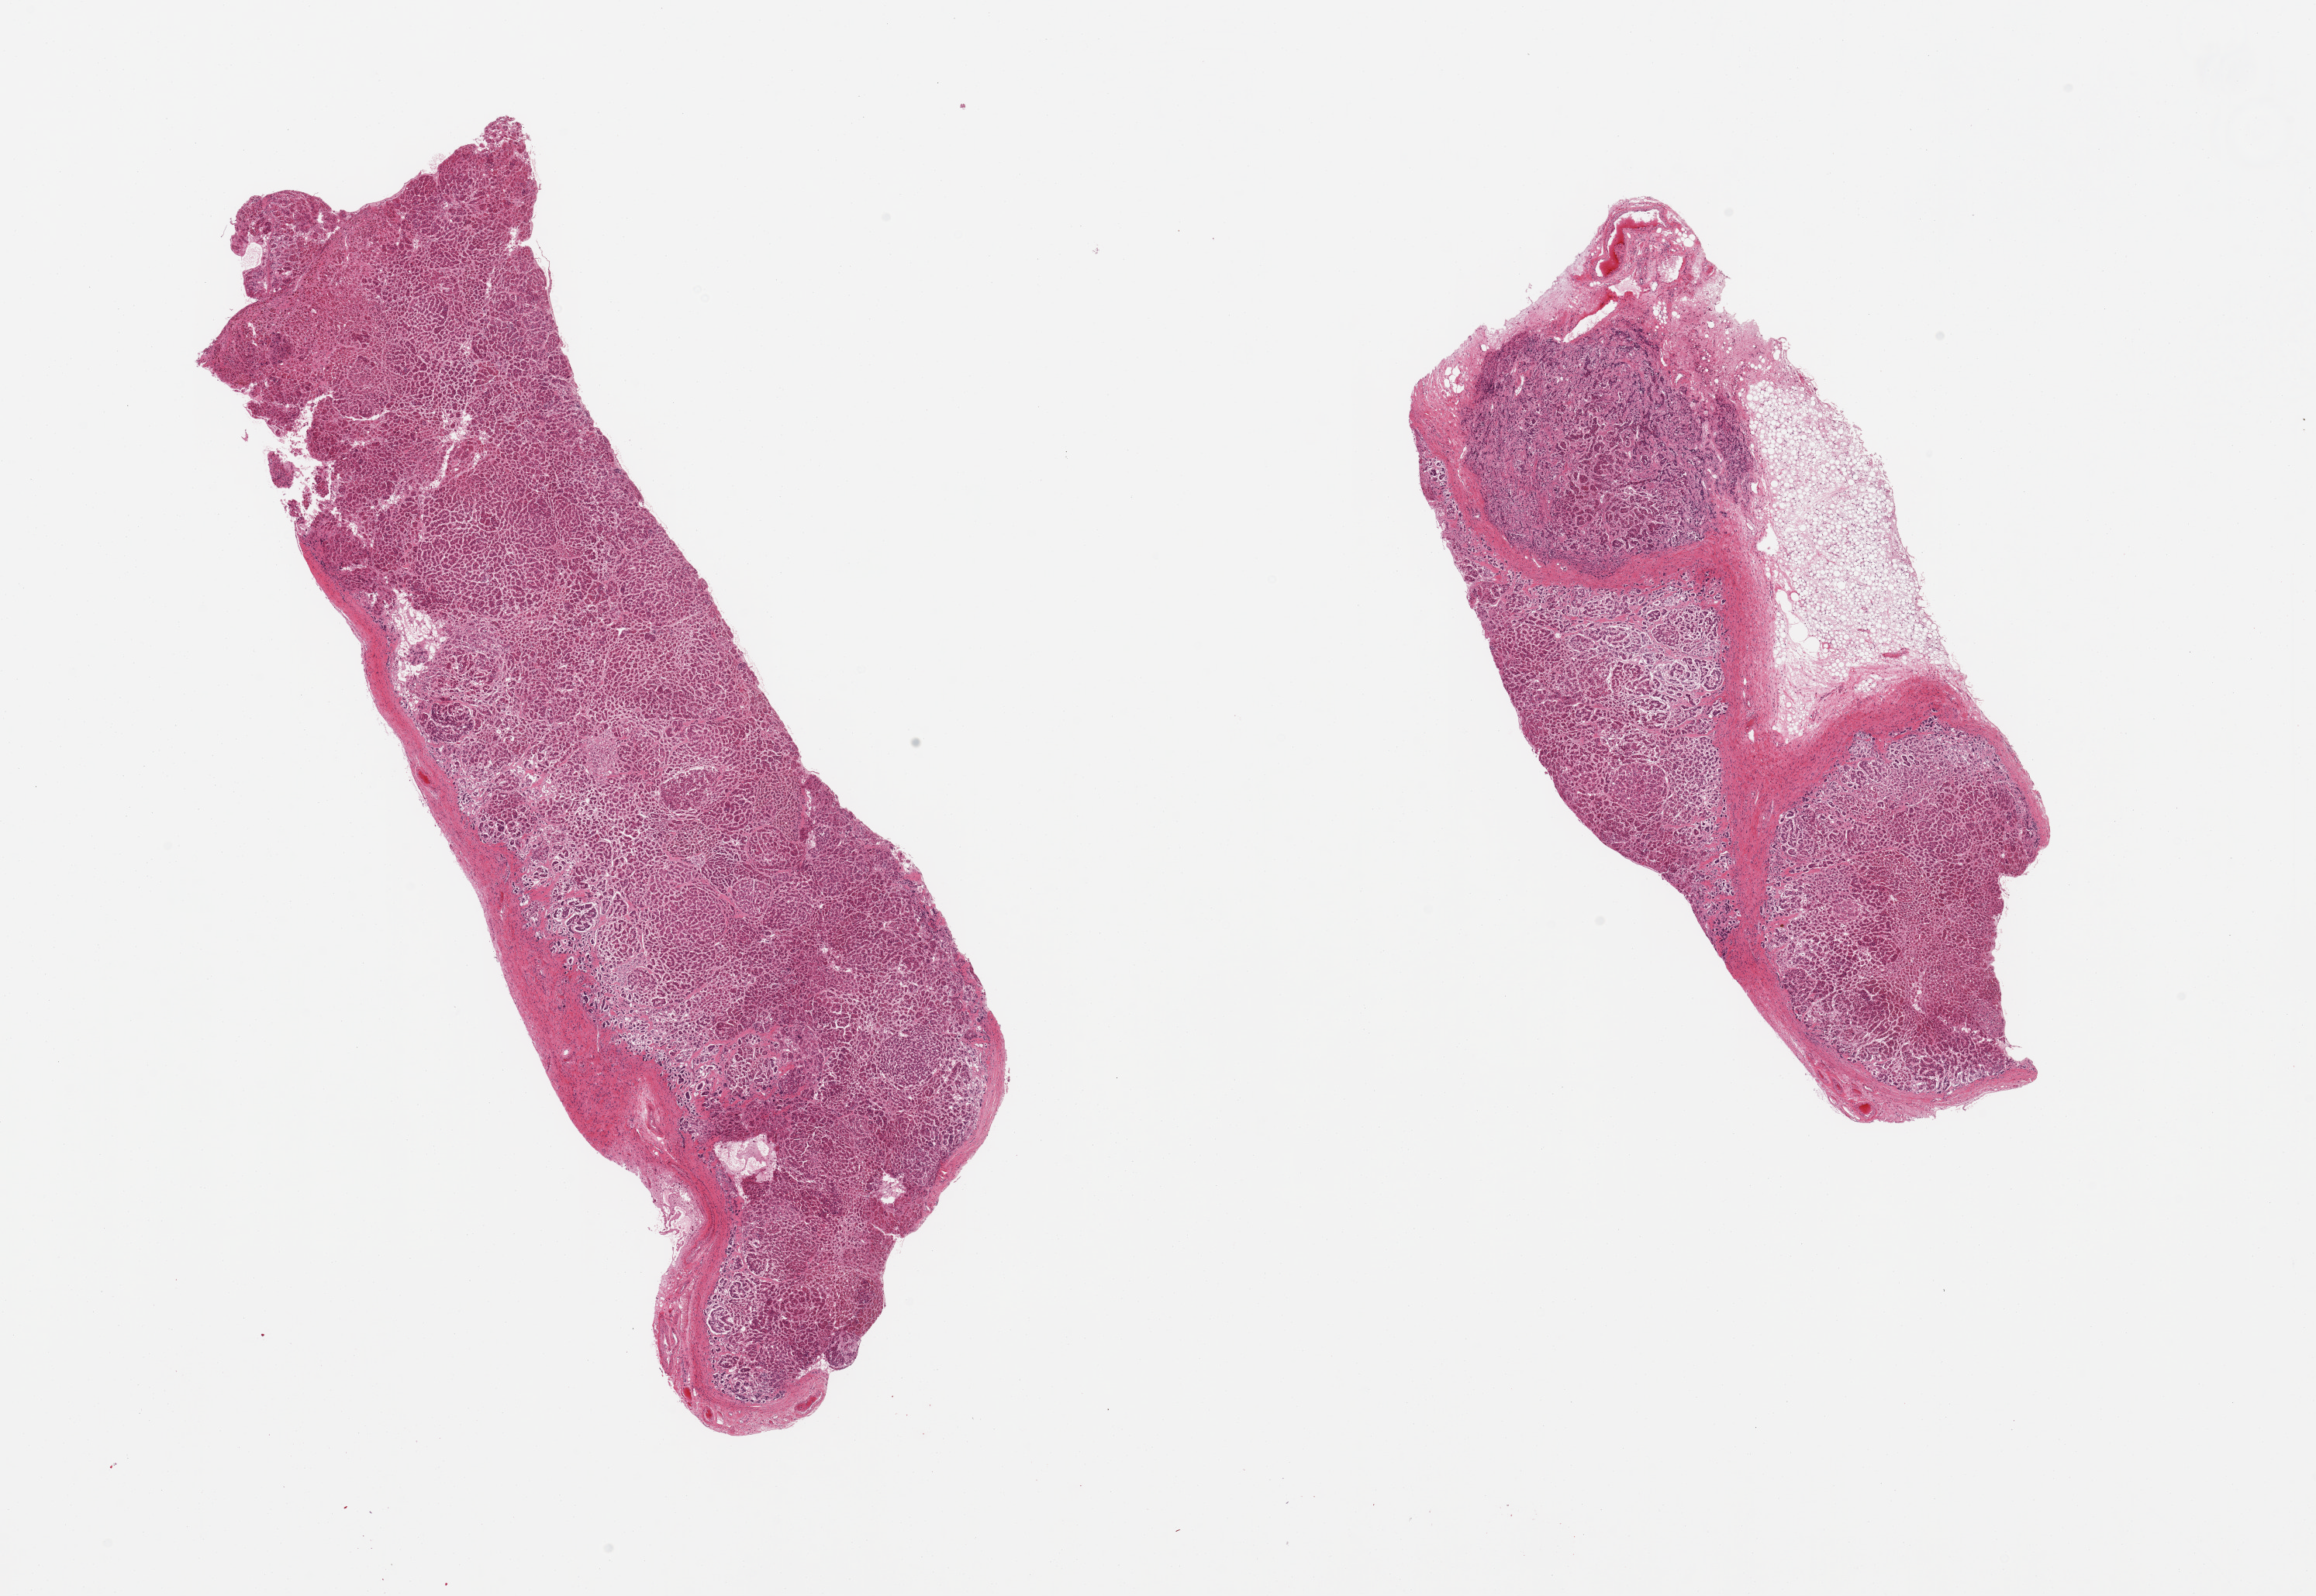
H&E whole-slide image — a low-resolution overview of the entire scanned area, about 23.6 x 16.3 mm, PAXgene-fixed, paraffin-embedded tissue, sampled site (target tissue): adrenal gland, donor tissue sample.
Review note (as recorded): 2 pieces; 1 has 20% fat.